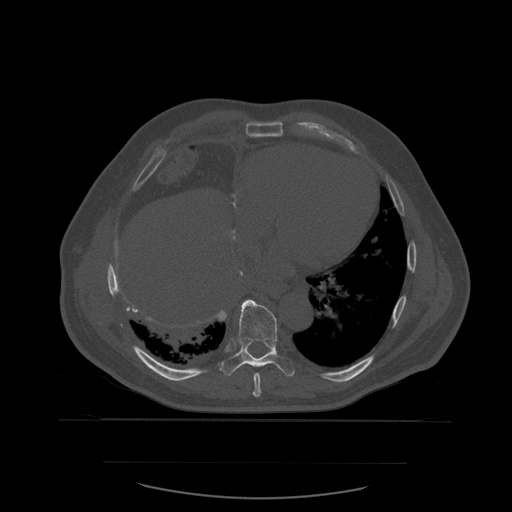
CT including the spine, one axial slice. Slice 344 of 590 in the series (ordered by position). Bone window (W 1800 / L 400 HU). 1.25 mm slice thickness. 512 × 512 image matrix. Patient age 71 years. From the clinical record (not read from this slice): primary cancer: lung.
Structures marked on this image (semi-automatic segmentation, software-assisted and operator-edited):
- T8 vertebra: bounding box <253,373,262,397> (left, top, right, bottom; pixels)
- T9 vertebra: <220,300,295,377>